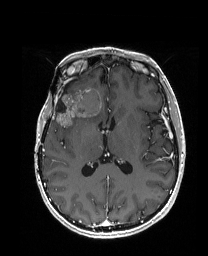
Brain MRI from a brain-tumour surgery series, one axial slice. Position 87 of 192 along the scan axis. T1-weighted post-contrast. 208 × 256 image matrix, field of view 203 × 250 mm. From the clinical record (not read from this slice): histopathology: Metastatic Carcinoma from Breast primary; tumour location: Right Frontal.
Annotated regions visible in this slice (expert manual segmentation):
- previous resection cavity: bounding box (x1, y1, x2, y2) in pixels: (56, 84, 69, 113)
- tumour: (55, 86, 104, 126)